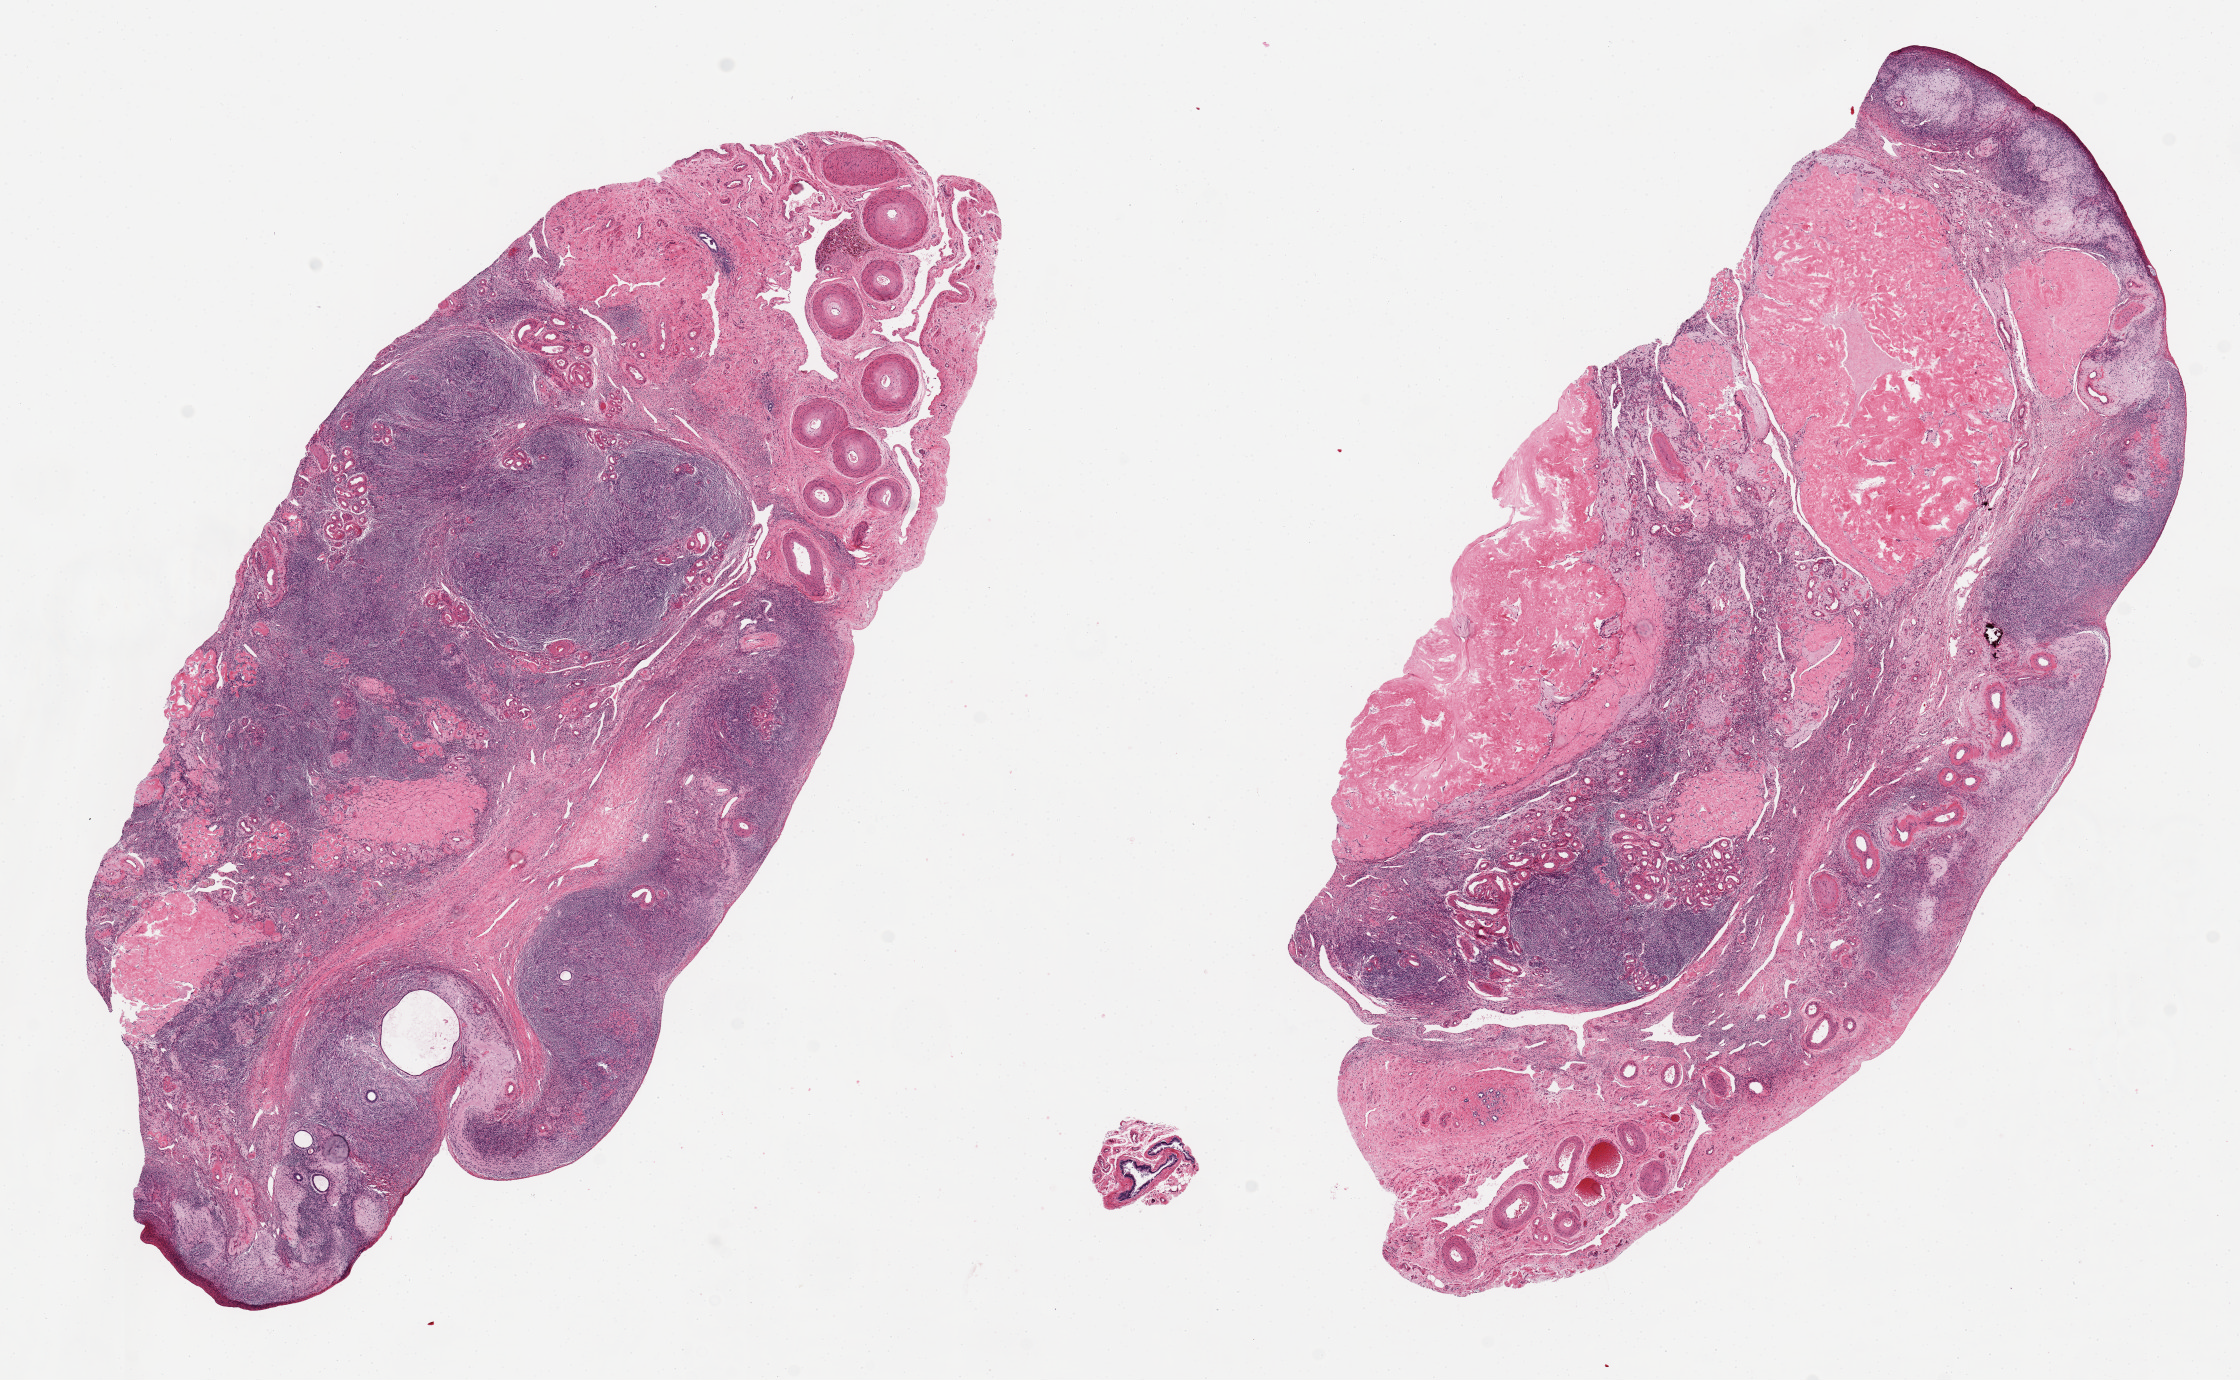
Digitized haematoxylin and eosin-stained section, low-resolution overview of the scanned area, about 17.7 x 10.9 mm. PAXgene-fixed paraffin-embedded (PFPE) section. Target tissue: ovary. Donor tissue sample. Donor sex: female.
Review note (as recorded): 2 pieces each ~10x4.5mm; corpora, no ova.